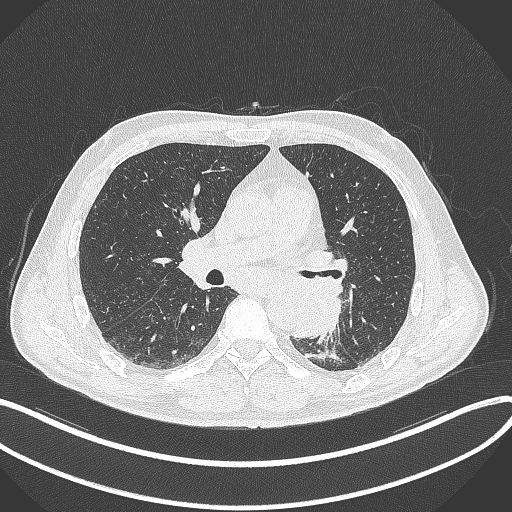
Chest CT, one axial slice; slice 185 of 329 in the series (ordered by position); reconstruction kernel B70f; 120 kVp; lung window (W 1500 / L -600 HU); 1 mm slice thickness; 512 × 512 image matrix, field of view 400 × 400 mm. Male patient, age 59 years. Case-level facts recorded for this patient, not image findings: clinical TNM (as recorded): T2a N2 M0.
Outlined on this slice (rectangle marked by the reading radiologist):
- lung tumour (recorded histology: squamous cell carcinoma): bounding box (x1, y1, x2, y2) in pixels: (290, 275, 347, 341)